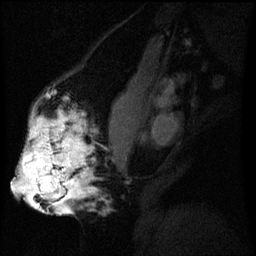
Breast MRI (dynamic contrast-enhanced), one sagittal slice. Slice 26 of 60 in the series (ordered by position). Dynamic contrast-enhanced series, image 2 of 3 at this slice position (ordered by acquisition). 1.5 T. TE 4.2 ms, TR 8 ms. 2.2 mm slice thickness. 256 × 256 image matrix. Patient: female, 50 years.
Annotated regions visible in this slice (semi-automatic segmentation, software-assisted and operator-edited):
- analysis volume of interest (the breast-tissue region the enhancement analysis was run in; not a lesion): box from (x=19, y=112) to (x=96, y=211) px
- tumour enhancement mask (voxels above the 70 % enhancement threshold inside the analysis volume of interest): (x=19, y=116)–(x=89, y=211)